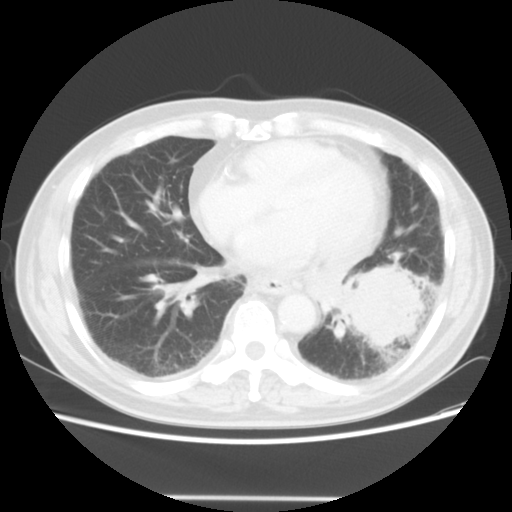
Chest CT, one axial slice; slice 18 of 56 in the series (ordered by position); reconstruction kernel STANDARD; 140 kVp; lung window (W 1500 / L -600 HU); 5 mm slice thickness; 512 × 512 image matrix, field of view 360 × 360 mm. Male patient, age 66 years. From the clinical record (not read from this slice): clinical TNM (as recorded): T4 N3 M0; histopathological grade: G3.
Structures marked on this image (bounding box drawn by a radiologist):
- lung tumour (recorded histology: small cell carcinoma): bounding box <333,258,441,356> (left, top, right, bottom; pixels)